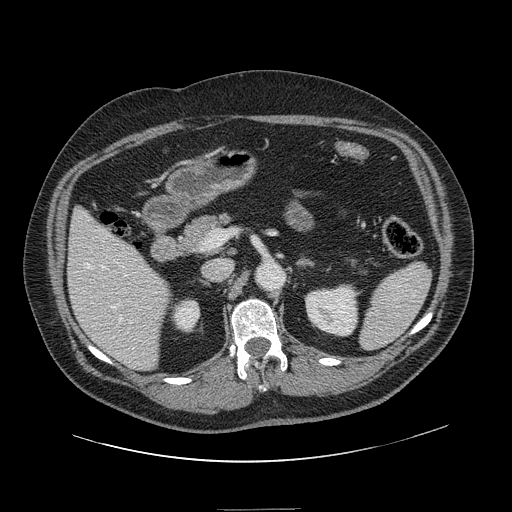
Contrast-enhanced abdominal CT, one axial slice. Slice 69 of 154 in the series (ordered by position). 120 kVp. Intravenous contrast given. Soft-tissue window (W 400 / L 40 HU). 2.5 mm slice thickness. 512 × 512 image matrix. Male patient, age 61 years. Case-level facts recorded for this patient, not image findings: diagnosis: colorectal cancer liver metastases, imaged before liver resection; multiple liver metastases: yes; largest metastasis: 2.6 cm; disease in both lobes: yes.
Outlined on this slice (outlined manually by an expert reader):
- hepatic veins: box from (x=85, y=263) to (x=134, y=349) px
- liver: (x=69, y=210)–(x=169, y=370)
- planned liver remnant (the part of the liver to remain after resection): (x=69, y=210)–(x=169, y=366)
- portal vein (with intrahepatic branches): (x=130, y=321)–(x=132, y=323)